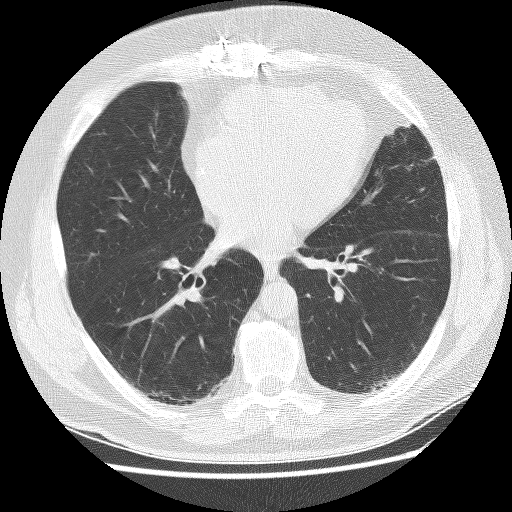
Axial slice from a low-dose chest CT screening exam, baseline annual screen, lung window (W 1500 / L -600 HU), 2.5 mm slice thickness, lung (sharp) reconstruction kernel (BONE), 120 kVp, slice 131 of 236 in the series. Male participant, aged 65 years at enrolment. Former smoker at enrolment.
Lesion marked by an expert reader, bounding box <354,371,395,407> (left, top, right, bottom; pixels). No non-calcified nodule or mass ≥4 mm was recorded by the screening reader at this exam. Participant outcome: lung cancer diagnosed 523 days after this screen — squamous cell carcinoma, NOS, left lower lobe, moderately differentiated (G2), stage IA (AJCC 6th edition), 20 mm at pathology.